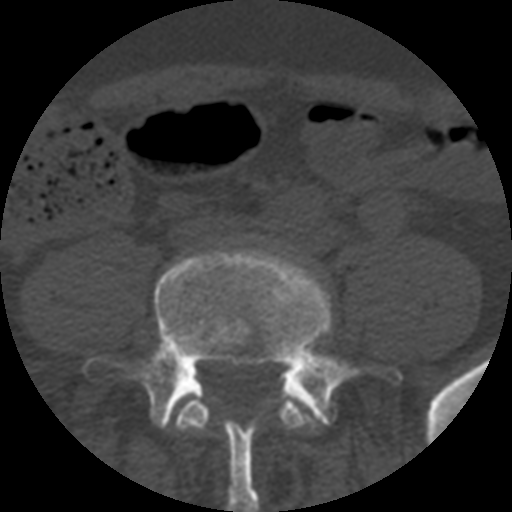
CT including the spine, one axial slice. Bone window (W 1800 / L 400 HU). 1.25 mm slice thickness. 512 × 512 image matrix, field of view 160 × 160 mm. Patient age 57 years. From the clinical record (not read from this slice): primary cancer: prostate.
Outlined on this slice (semi-automatic segmentation, software-assisted and operator-edited):
- L4 vertebra: bounding box (x1, y1, x2, y2) in pixels: (175, 391, 327, 431)
- L5 vertebra: (84, 249, 400, 512)